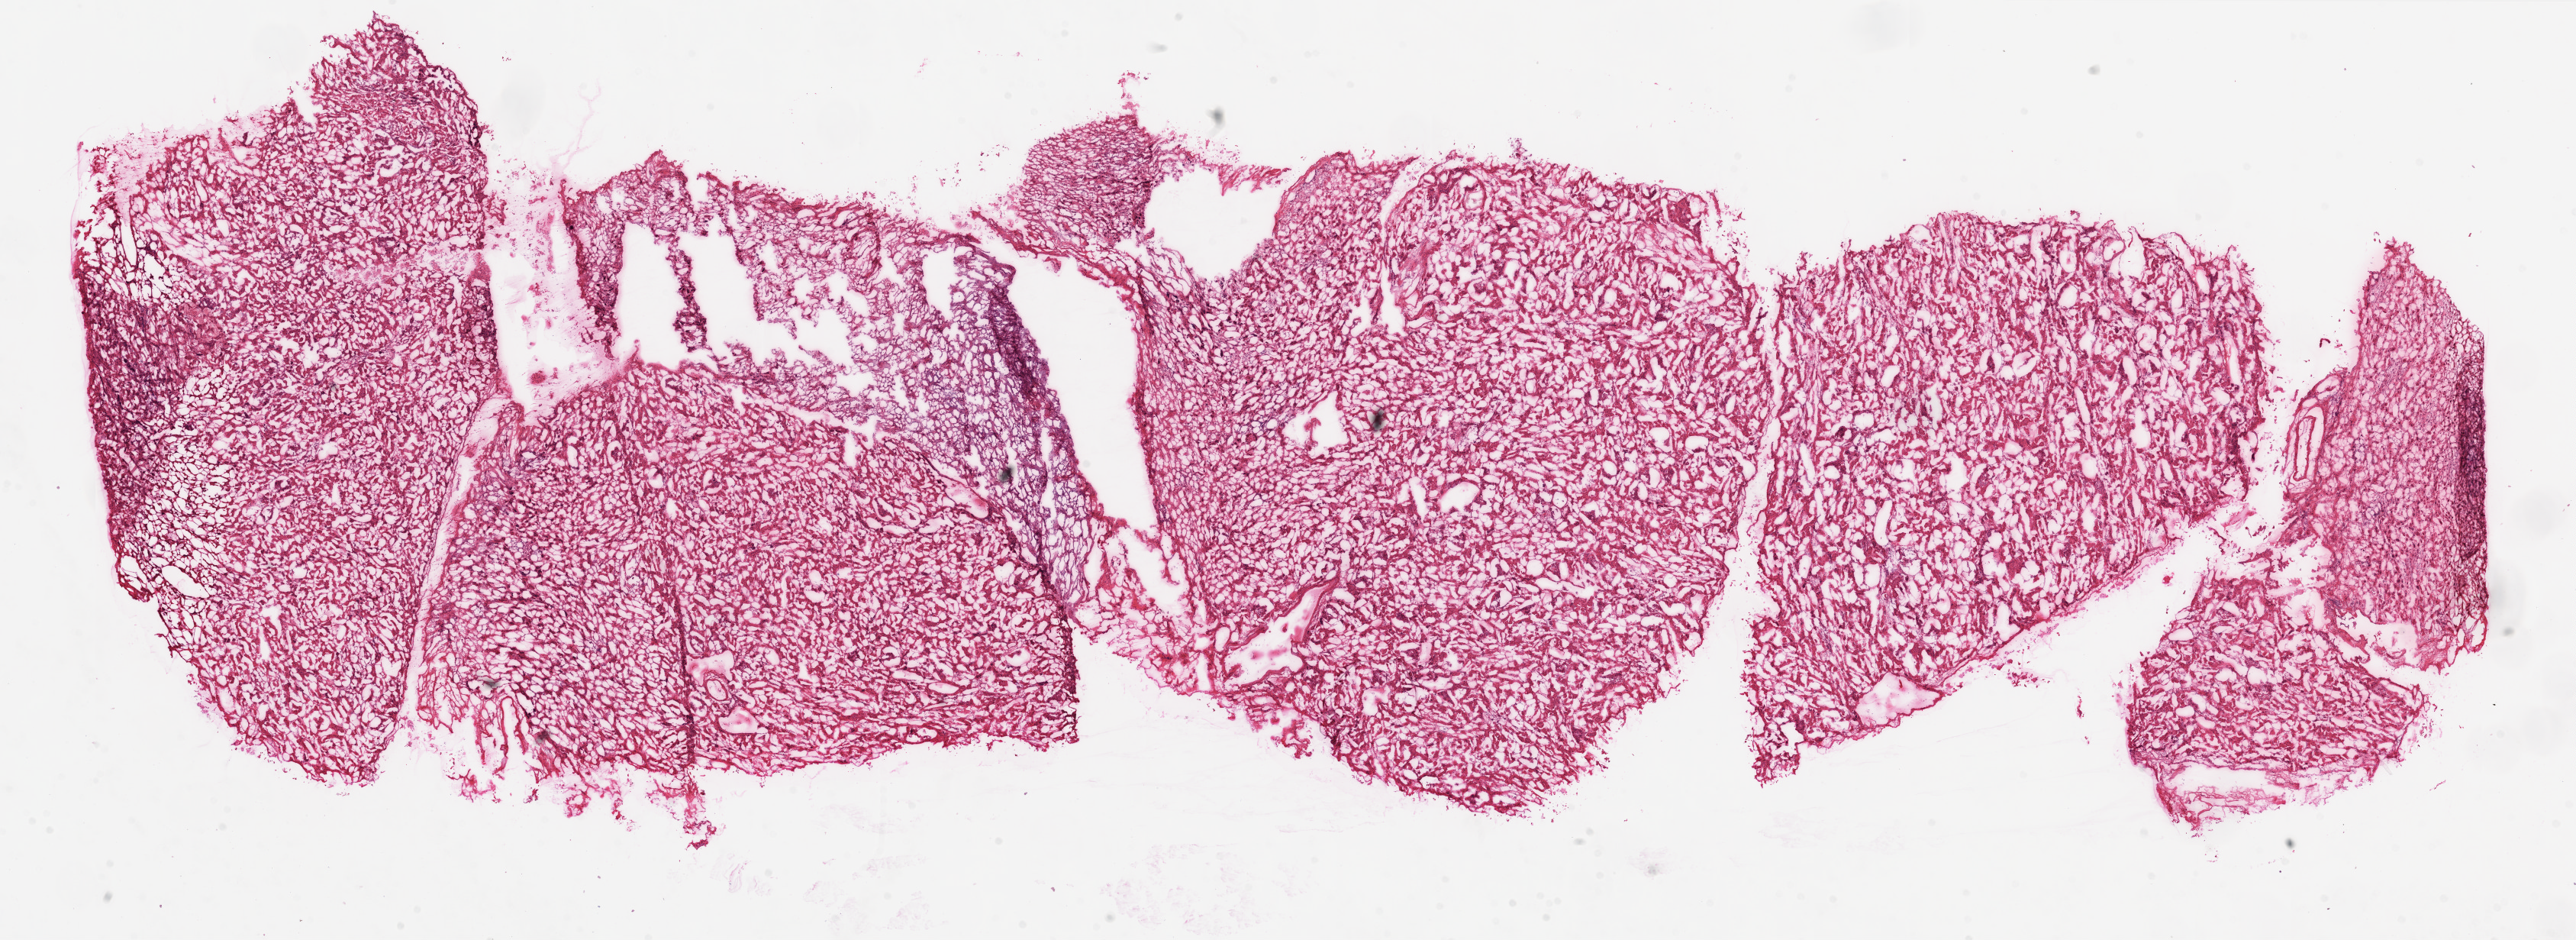
Whole-slide histology image, Hematoxylin and eosin (H&E) stained, a low-resolution overview of the entire scanned area, about 27.1 x 9.9 mm (slide scanned at 20x), frozen section from the top of the tissue portion, sample: solid tissue normal (non-tumour tissue), kidney. Patient: female, age at initial diagnosis 45 years.
This section: solid tissue normal (non-tumour) sample from the same patient. Patient diagnosis: Clear cell adenocarcinoma, NOS.